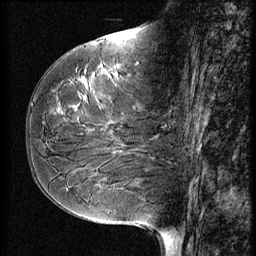
Breast MRI (dynamic contrast-enhanced), one sagittal slice; slice 27 of 56 in the series (ordered by position); 3 images stored at this slice position (order not interpretable as contrast timing); 1.5 T; TE 4.2 ms, TR 9 ms; 256 × 256 image matrix, field of view 180 × 180 mm. Patient: female, 51 years. From the clinical record (not read from this slice): setting: breast cancer imaged before/during neoadjuvant chemotherapy; receptor status: HR-positive, HER2-negative.
Annotated regions visible in this slice (semi-automatic segmentation, software-assisted and operator-edited):
- analysis volume of interest (the breast-tissue region the enhancement analysis was run in; not a lesion): box from (x=41, y=58) to (x=167, y=161) px
- tumour enhancement mask (voxels above the 140 % enhancement threshold inside the analysis volume of interest): (x=59, y=78)–(x=88, y=115)